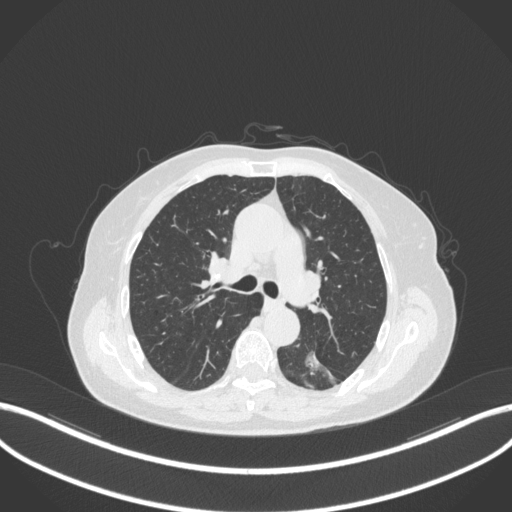
Chest CT, one axial slice. Slice 194 of 352 in the series (ordered by position). Reconstruction kernel B31f. Lung window (W 1500 / L -600 HU). 512 × 512 image matrix, field of view 400 × 400 mm. Patient: female, 70 years. Case-level facts recorded for this patient, not image findings: clinical TNM (as recorded): T1c N0 M0.
Outlined on this slice (rectangle marked by the reading radiologist):
- lung tumour (recorded histology: adenocarcinoma): bounding box [x1, y1, x2, y2] px = [298, 345, 326, 376]